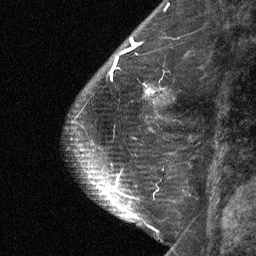
Breast MRI (dynamic contrast-enhanced), one sagittal slice. Slice 20 of 64 in the series (ordered by position). Dynamic contrast-enhanced study with each time point stored as its own series, time point 2 of 3 at this slice position (early post-contrast, ordered by acquisition time). 1.5 T. TE 4.8 ms, TR 27 ms. 2 mm slice thickness. 256 × 256 image matrix, field of view 180 × 180 mm. Female patient, age 59 years. Case-level facts recorded for this patient, not image findings: setting: breast cancer imaged before/during neoadjuvant chemotherapy; receptor status: triple-negative.
Structures marked on this image (semi-automatic segmentation, software-assisted and operator-edited):
- analysis volume of interest (the breast-tissue region the enhancement analysis was run in; not a lesion): bounding box (x1, y1, x2, y2) in pixels: (122, 58, 176, 109)
- tumour enhancement mask (voxels above the 90 % enhancement threshold inside the analysis volume of interest): (145, 86, 154, 94)